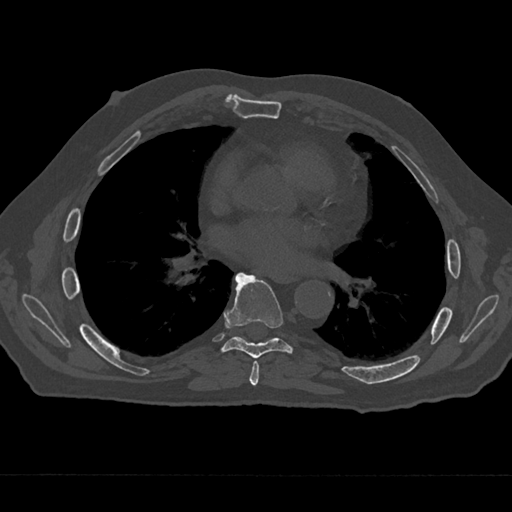
CT including the spine, one axial slice; slice 369 of 797 in the series (ordered by position); reconstruction kernel Br40s/3; 120 kVp; bone window (W 1800 / L 400 HU); 0.5 mm slice thickness; 512 × 512 image matrix, field of view 377 × 377 mm. Patient: male, 75 years. Case-level facts recorded for this patient, not image findings: primary cancer: renal.
Outlined on this slice (semi-automatic segmentation, software-assisted and operator-edited):
- T6 vertebra: bounding box <249,361,259,386> (left, top, right, bottom; pixels)
- T7 vertebra: <215,272,297,359>